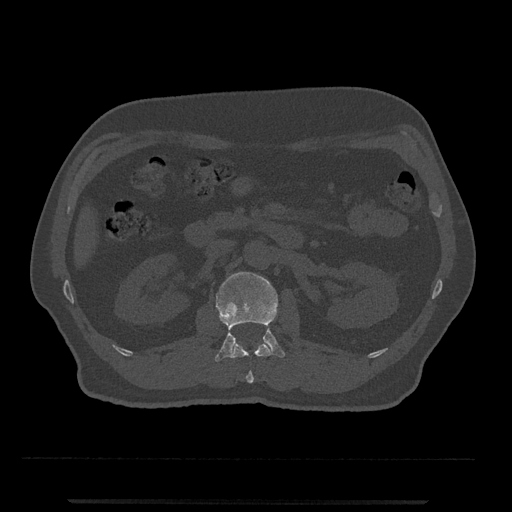
CT including the spine, one axial slice; position 294 of 797 along the scan axis; reconstruction kernel Br40s/3; 120 kVp; bone window (W 1800 / L 400 HU); 0.5 mm slice thickness; 512 × 512 image matrix. Patient: male, 63 years. From the clinical record (not read from this slice): primary cancer: prostate.
Structures marked on this image (semi-automatic segmentation, software-assisted and operator-edited):
- L1 vertebra: bounding box (x1, y1, x2, y2) in pixels: (230, 343, 273, 383)
- L2 vertebra: (215, 272, 285, 362)